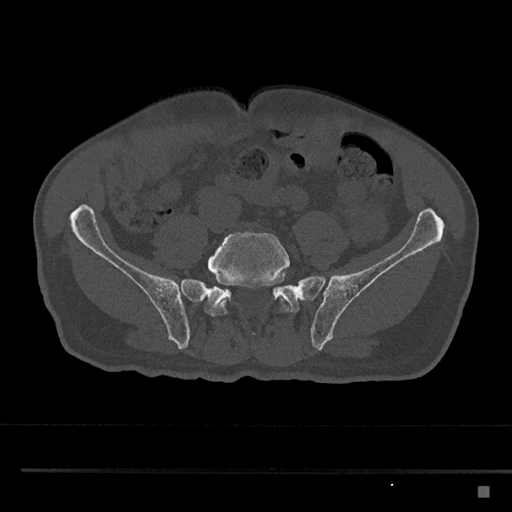
CT including the spine, one axial slice. Slice 562 of 797 in the series (ordered by position). Bone window (W 1800 / L 400 HU). 0.5 mm slice thickness. 512 × 512 image matrix, field of view 391 × 391 mm. Patient: male, 59 years. From the clinical record (not read from this slice): primary cancer: prostate.
Annotated regions visible in this slice (semi-automatic segmentation, software-assisted and operator-edited):
- L5 vertebra: bounding box [x1, y1, x2, y2] px = [208, 232, 291, 317]